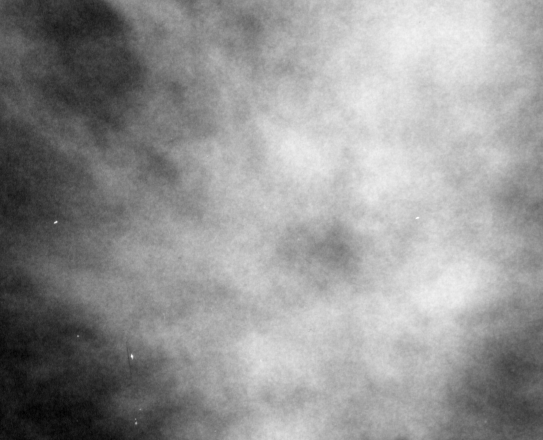
Crop from a digitized film mammogram around one marked abnormality, left breast, CC view.
Mass, shape irregular, margins spiculated; BI-RADS assessment category 5; subtlety rating 5 on a 1 (subtle) to 5 (obvious) scale; pathology result (as recorded, not read from the image): malignant.